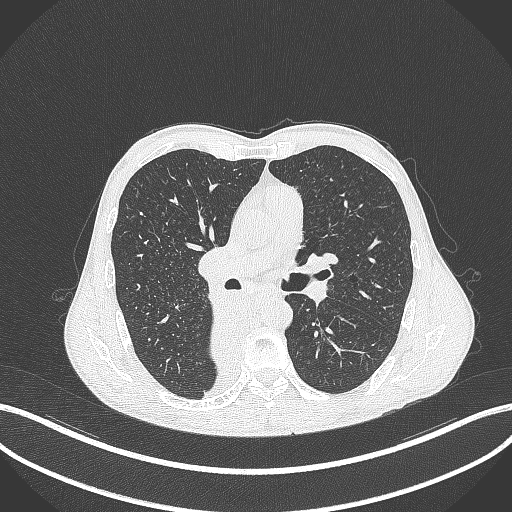
Chest CT, one axial slice; reconstruction kernel B70f; 120 kVp; lung window (W 1500 / L -600 HU); 512 × 512 image matrix, field of view 400 × 400 mm. Male patient, age 58 years. Case-level facts recorded for this patient, not image findings: clinical TNM (as recorded): T3 N1 M1.
Annotated regions visible in this slice (rectangle marked by the reading radiologist):
- lung tumour (recorded histology: squamous cell carcinoma): bounding box [x1, y1, x2, y2] px = [203, 296, 254, 382]